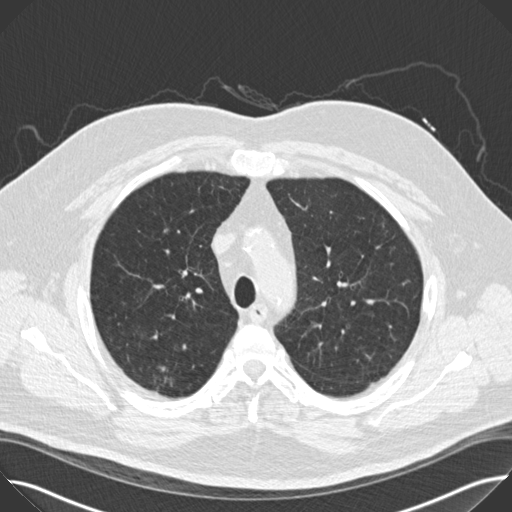
Chest CT (low-dose screening protocol), one axial image; baseline screening round; lung window (W 1500 / L -600 HU); 120 kVp; 512 × 512 image matrix. Male participant, aged 65 years at enrolment. Former smoker at enrolment.
Expert-annotated lung lesion, bounding box [x1, y1, x2, y2] px = [148, 360, 190, 419]. The screening reader recorded 2 non-calcified nodules or masses ≥4 mm on this exam (right upper lobe, right upper lobe); which of them this box marks is not recorded. Official screen result: positive, change unspecified: nodule(s) >= 4 mm or enlarging nodule(s), mass(es), or other non-specific abnormalities suspicious for lung cancer. Participant outcome: lung cancer diagnosed 47 days after this screen — bronchiolo-alveolar adenocarcinoma, NOS, right upper lobe, moderately differentiated (G2), stage IIA (AJCC 6th edition), 14 mm at pathology.